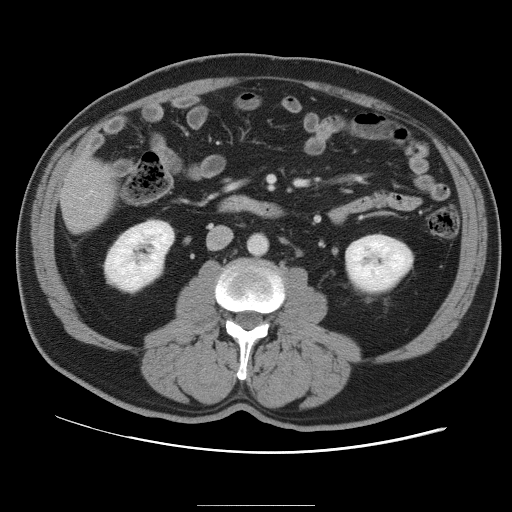
Contrast-enhanced abdominal CT, one axial slice. Position 25 of 105 along the scan axis. 120 kVp. Soft-tissue window (W 400 / L 40 HU). 5 mm slice thickness. 512 × 512 image matrix, field of view 399 × 399 mm. Male patient, age 64 years. Case-level facts recorded for this patient, not image findings: diagnosis: colorectal cancer liver metastases, imaged before liver resection; multiple liver metastases: yes; largest metastasis: 3 cm.
Structures marked on this image (expert manual segmentation):
- liver: bounding box [x1, y1, x2, y2] px = [60, 161, 115, 232]
- planned liver remnant (the part of the liver to remain after resection): [60, 161, 116, 227]